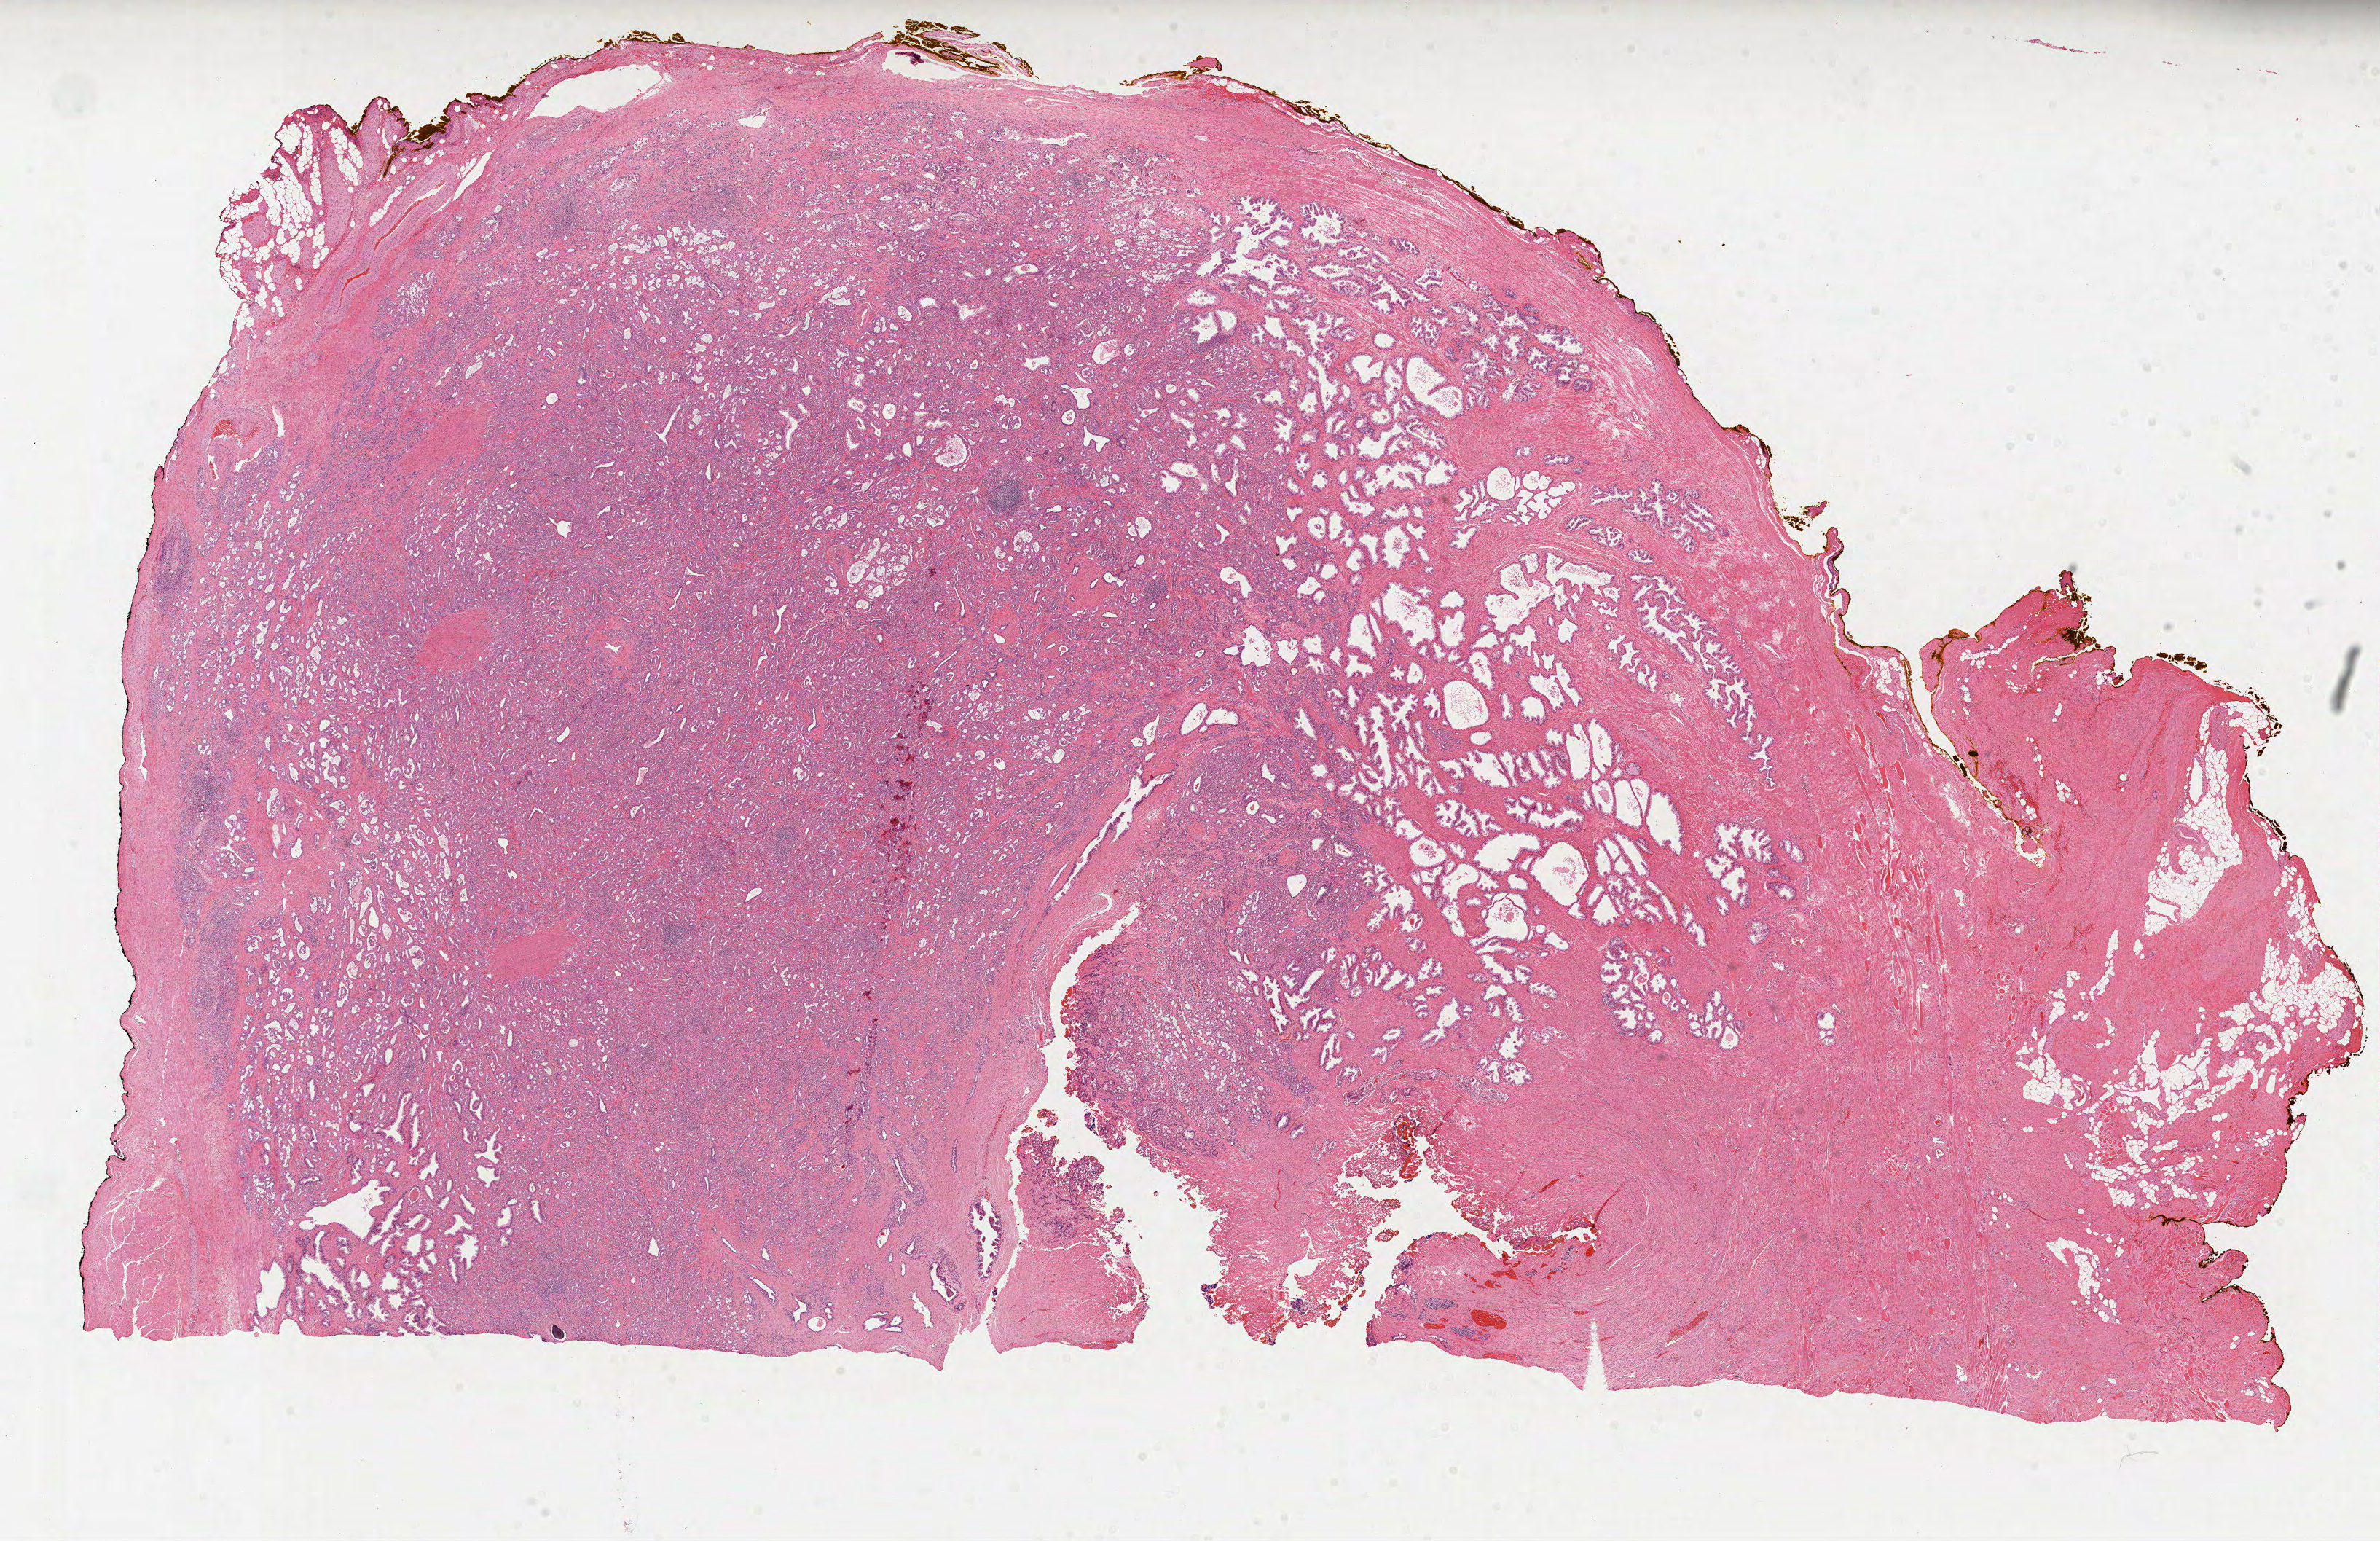
Whole-slide histology image, H&E — low-resolution overview of the scanned area, about 26.3 x 17.1 mm (acquisition: 40x scan); formalin-fixed paraffin-embedded (FFPE) diagnostic section; primary tumour sample from the prostate. Male, age 53 years at initial diagnosis. Gleason score: 7 (3+4).
Laterality: bilateral. Lymph nodes positive (case pathology): 0 of 14 examined. Histologic diagnosis: Acinar cell carcinoma (prostate gland).